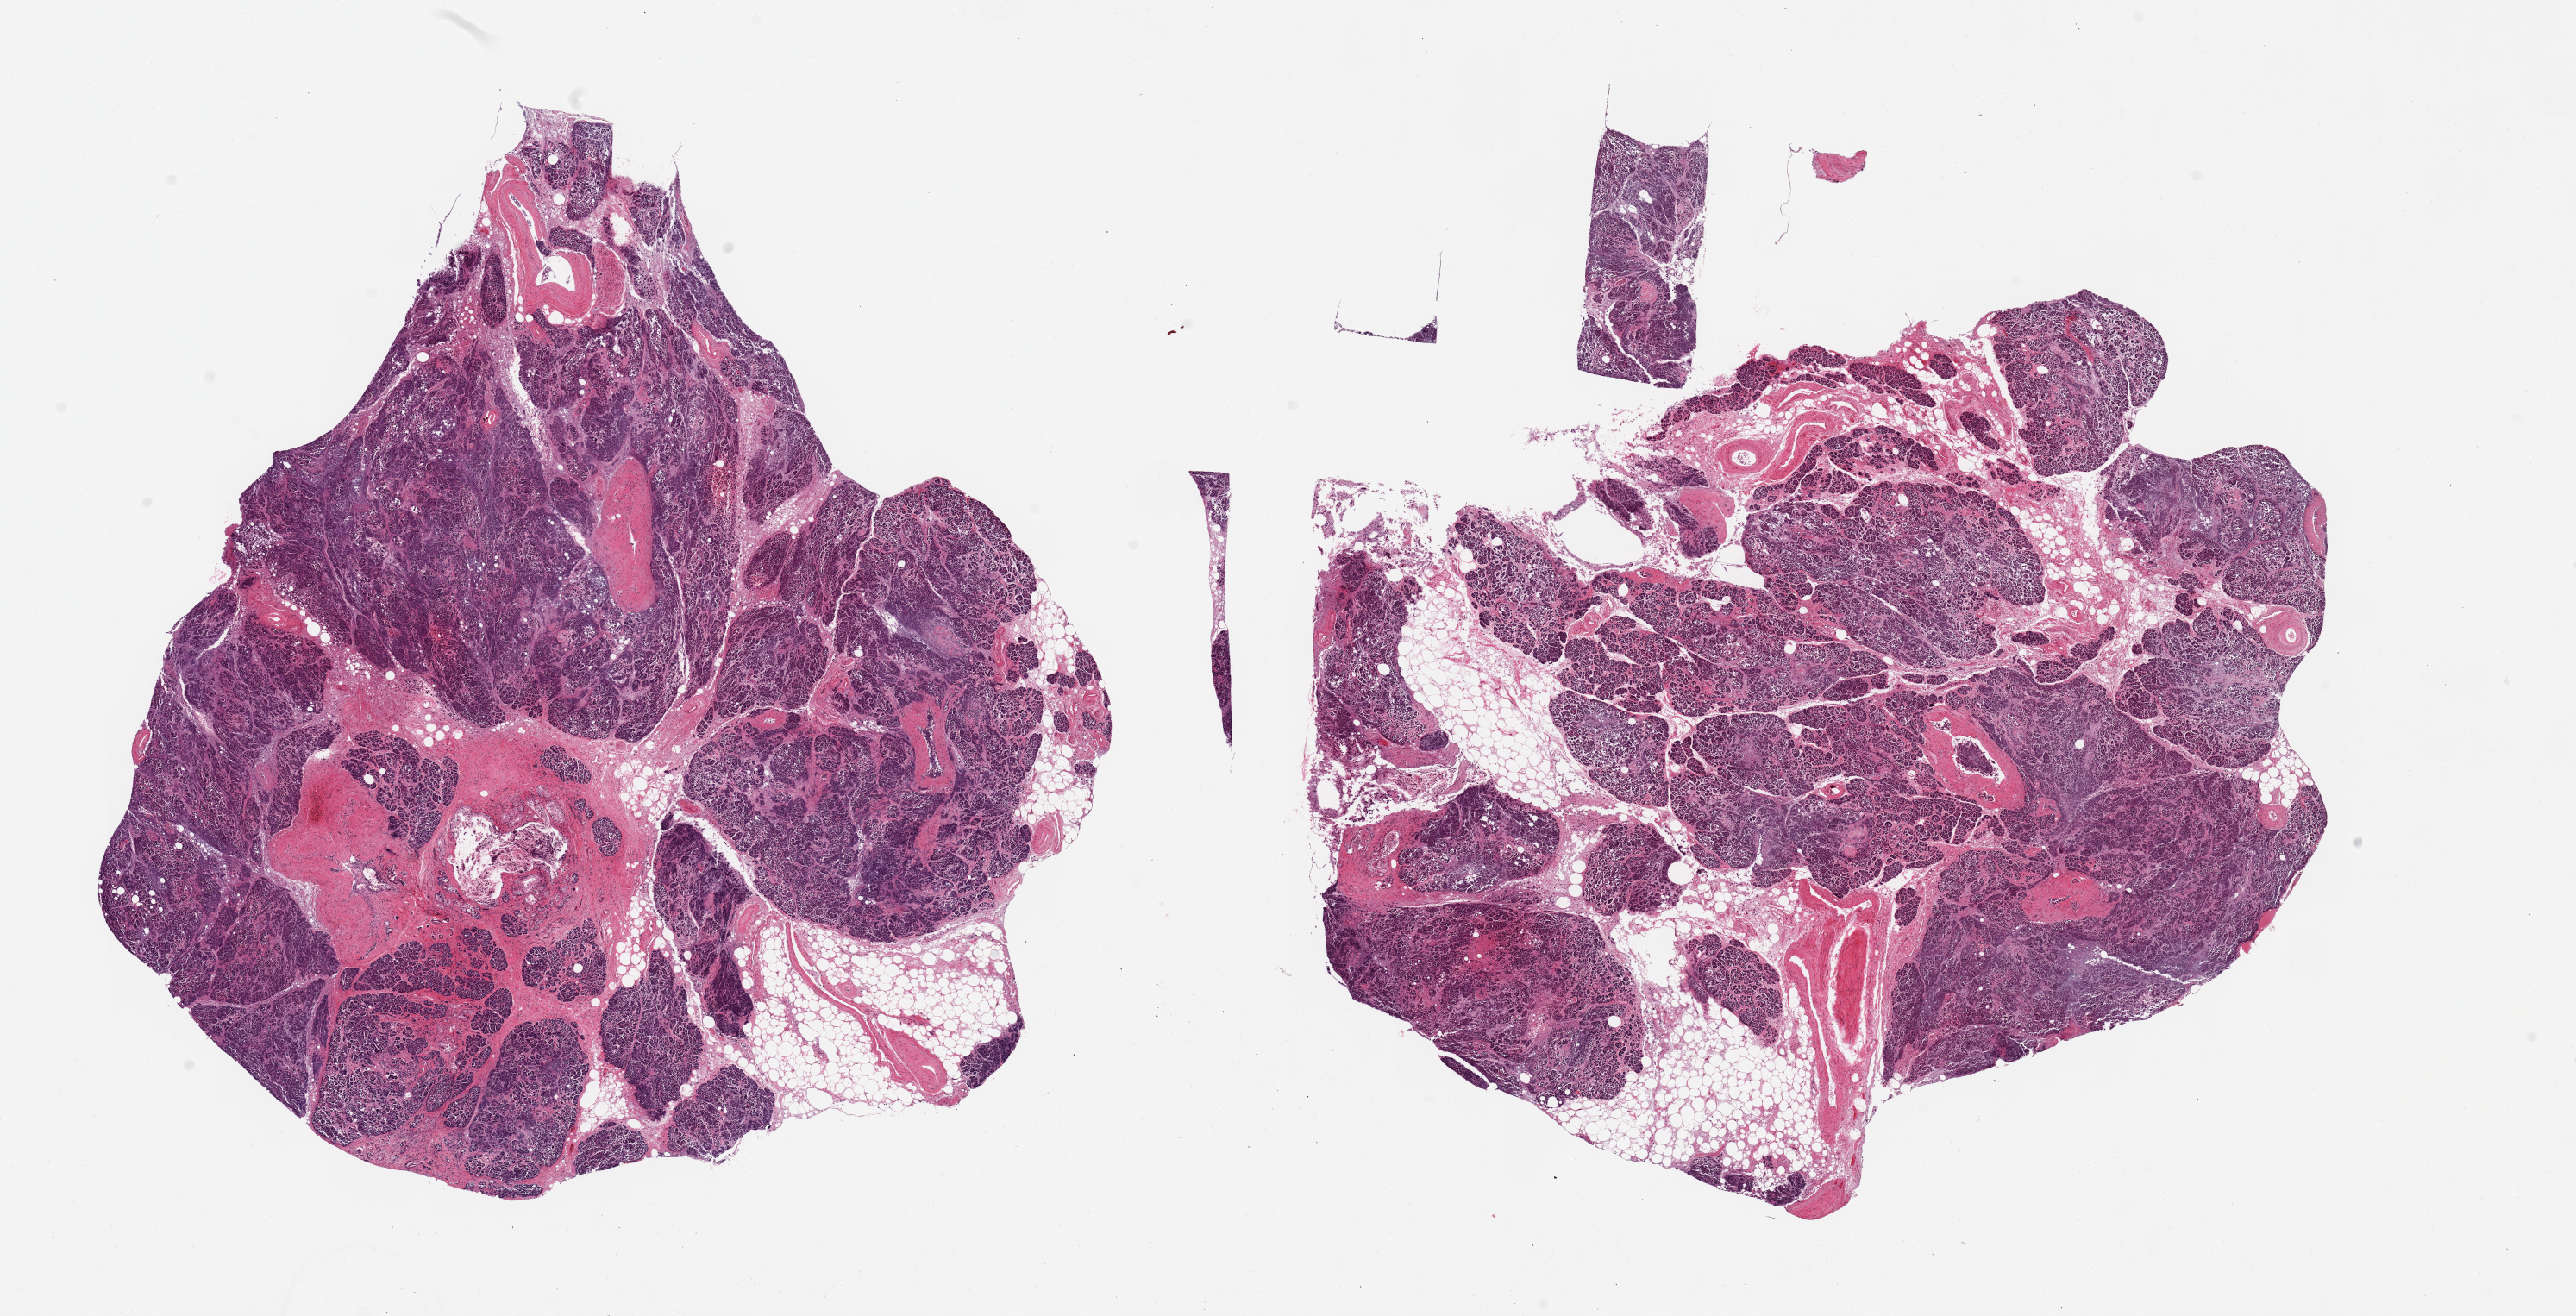
Haematoxylin and eosin whole-slide image — low-resolution overview of the scanned area, about 23.6 x 12.1 mm. PAXgene-fixed paraffin-embedded (PFPE) section. Sampled site (target tissue): pancreas. Donor tissue sample.
Pathologist's review note for this sample: 2 pieces; moderate to severe autolysis; 10-20% external/internal fat, focal fibrosis and atrophy, few foci of amyloid-like material (?degenerated islets with changes secondary to diabetes).